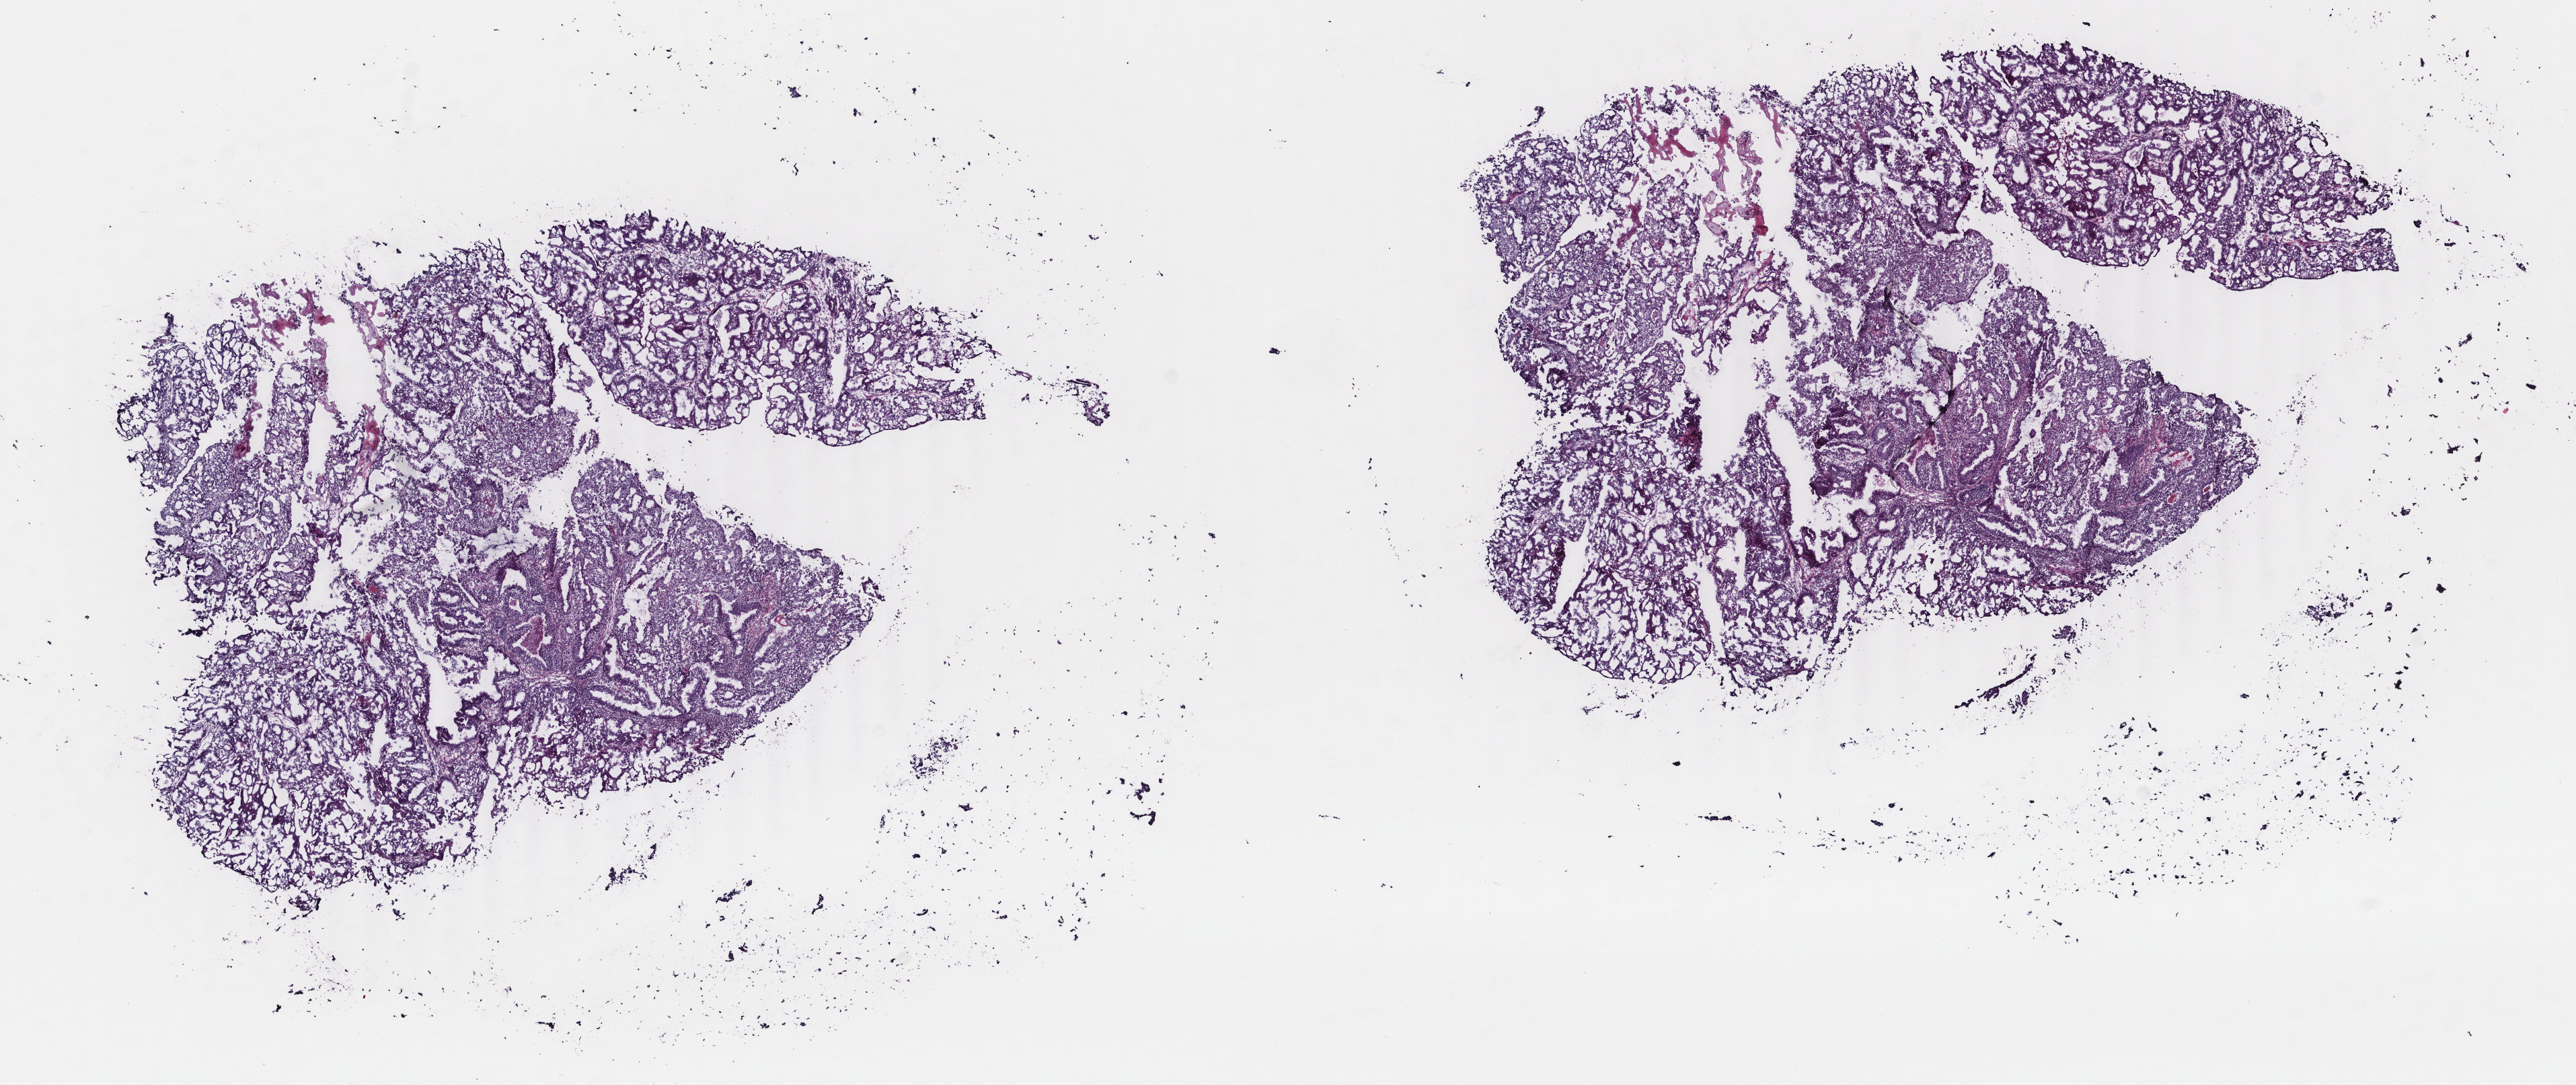
Hematoxylin and eosin (H&E) stained whole-slide image — whole scanned area (about 15.2 x 6.4 mm, from a 40x scan) shown as a low-resolution overview; frozen section from the top of the tissue portion; sample: primary tumour, uterus. Female patient; age at initial diagnosis 64 years. Pathologist review of this section (percent, as recorded): tumour cells 95%, tumour nuclei 95%.
Diagnosis: Endometrioid adenocarcinoma, NOS.